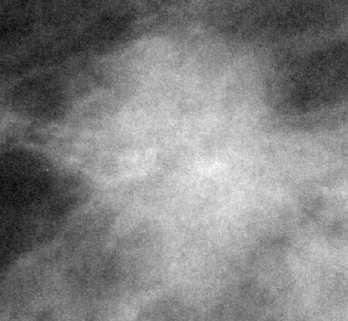
Crop from a digitized film mammogram around one marked abnormality, right breast, CC view, BI-RADS breast density category 2 (scale 1–4).
Mass, shape irregular, margins microlobulated; BI-RADS assessment category 5; pathology (as recorded): malignant.